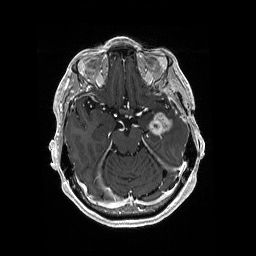
Brain MRI from a brain-tumour surgery series, one axial slice; T1-weighted post-contrast; 1 mm slice thickness; 256 × 256 image matrix, field of view 256 × 256 mm. From the clinical record (not read from this slice): histopathology: Glioblastoma; WHO grade: 4; IDH mutation: no; tumour location: Left Medial Temporal.
Outlined on this slice (outlined manually by an expert reader):
- tumour: bounding box <147,111,174,137> (left, top, right, bottom; pixels)